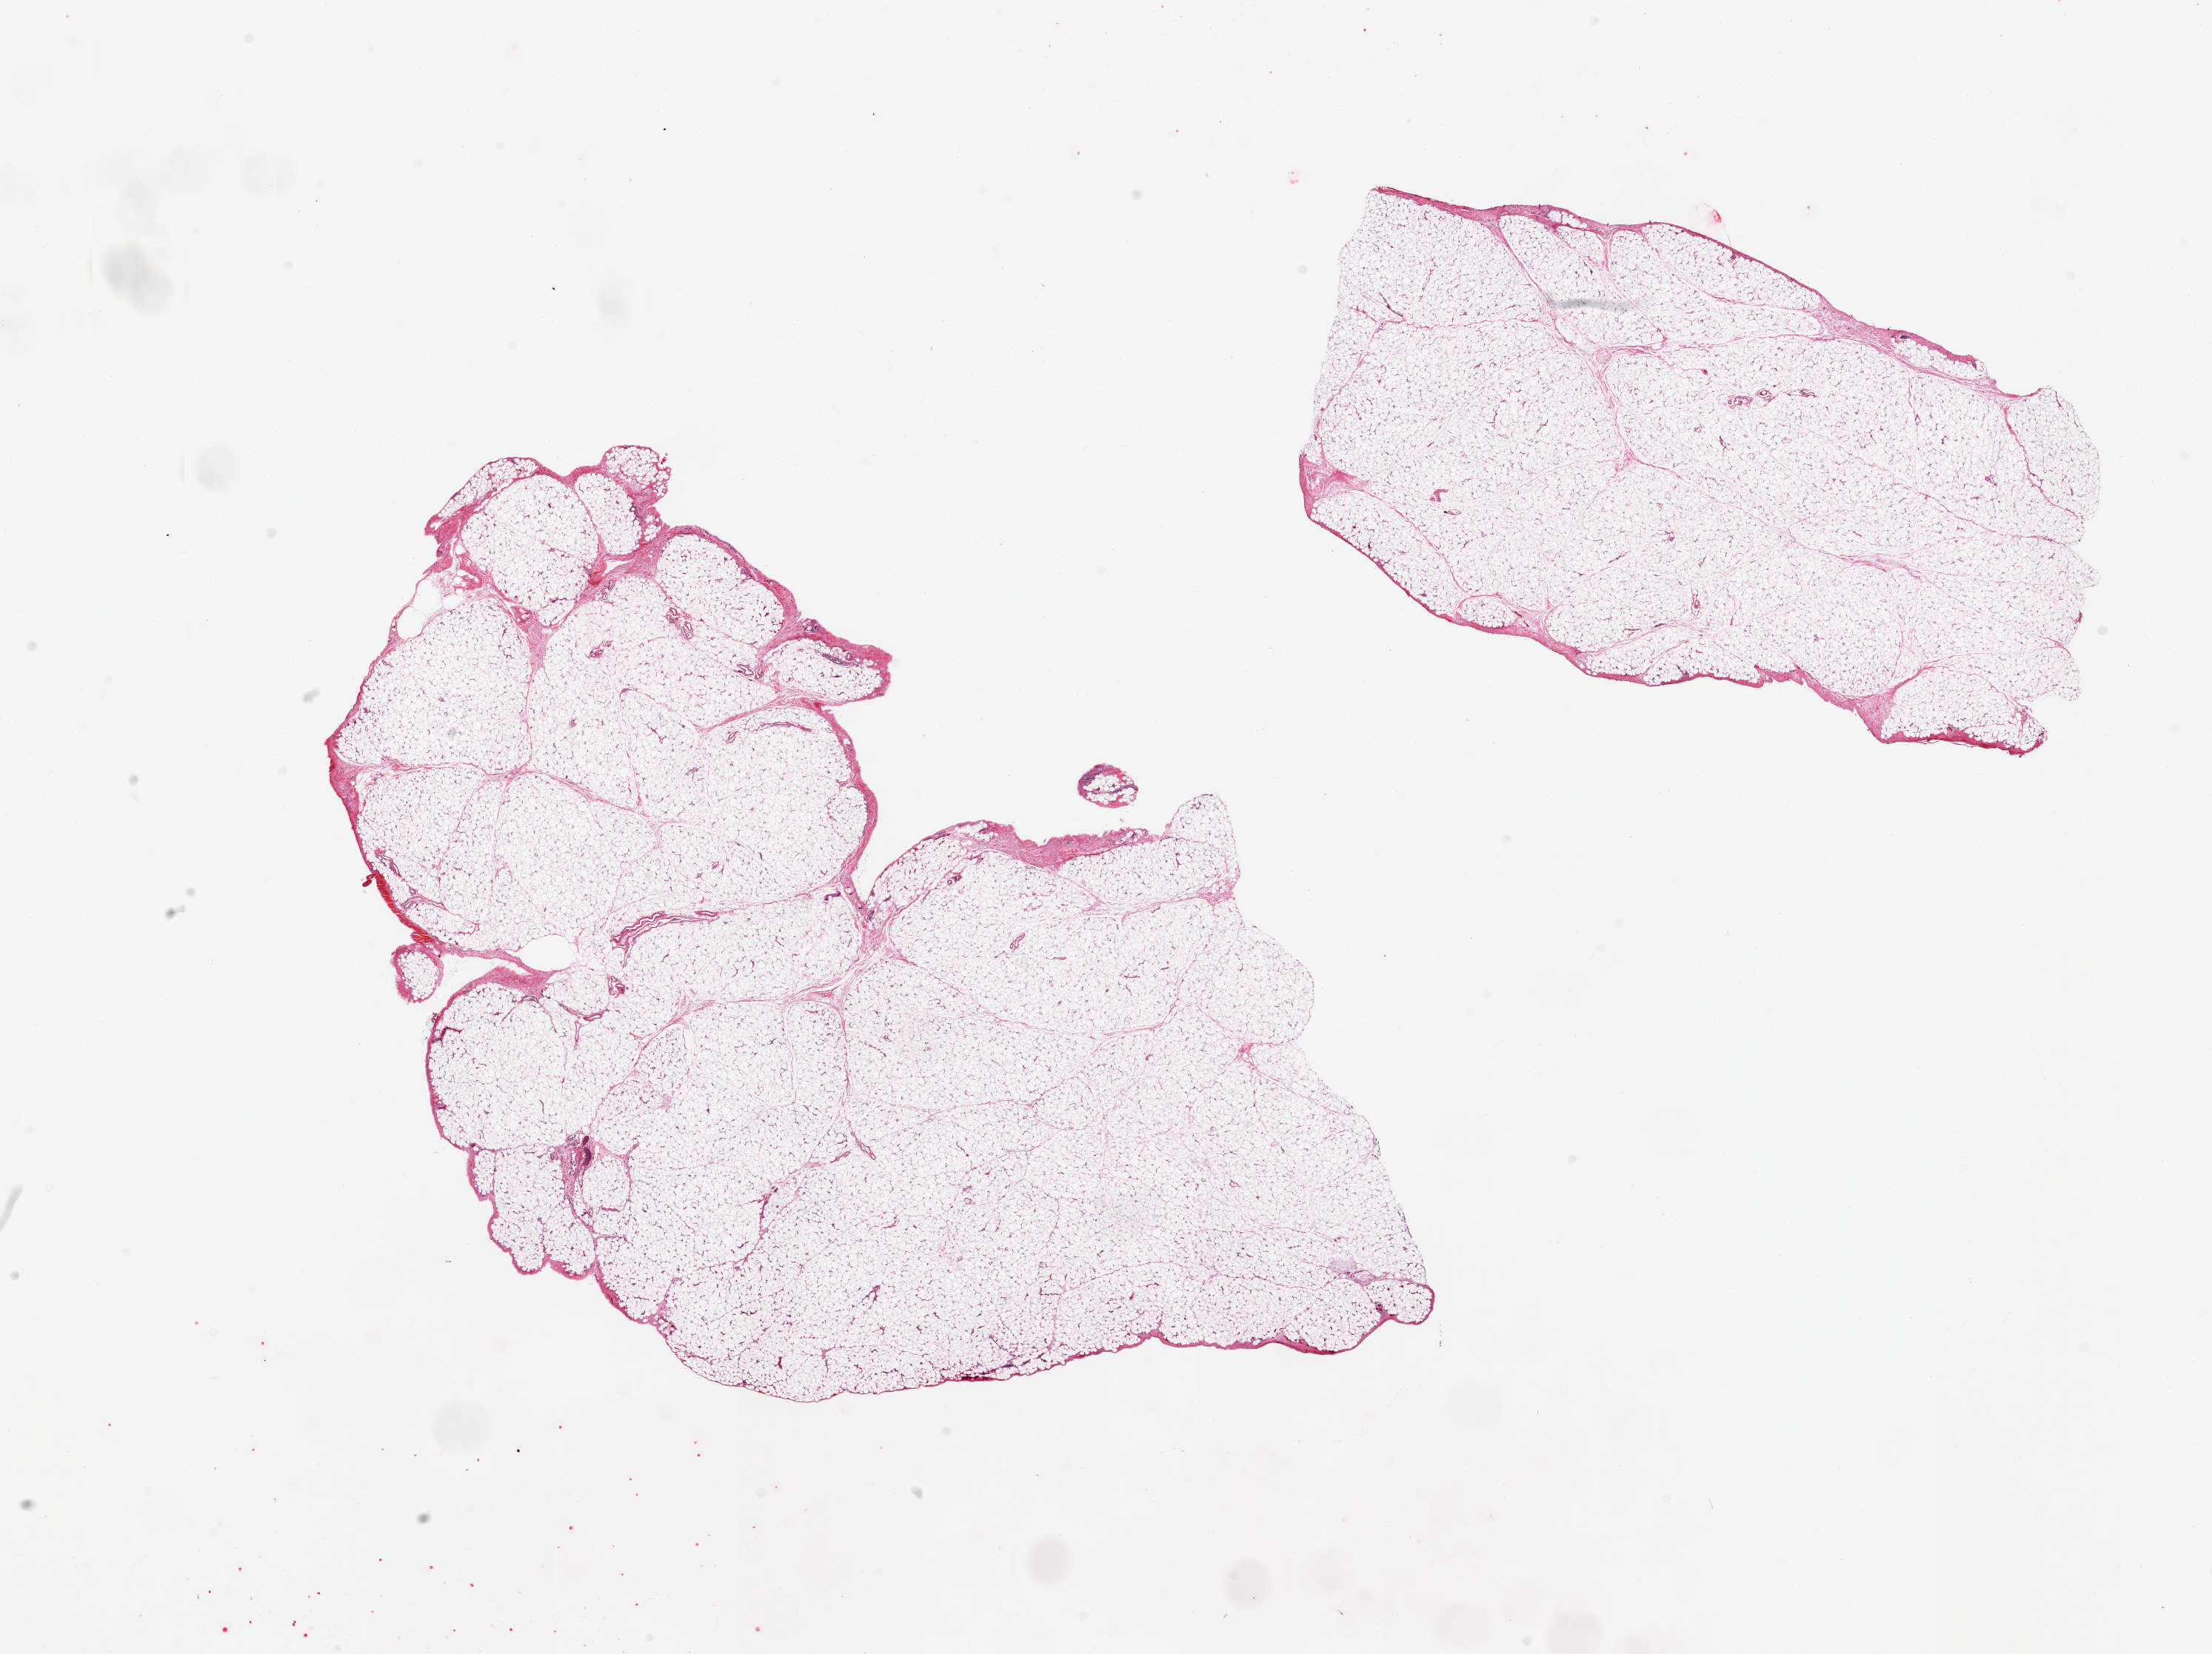
Hematoxylin and eosin (H&E) whole-slide image, brightfield — shown as a low-resolution overview of the whole scanned area (about 23.6 x 17.7 mm), PAXgene-fixed paraffin-embedded (PFPE) section, section of omentum (target tissue), donor tissue sample. Donor sex: male.
Reviewer comment on this tissue sample: 2 pieces; lobulated mature adipose tissue and fibrovascular component.